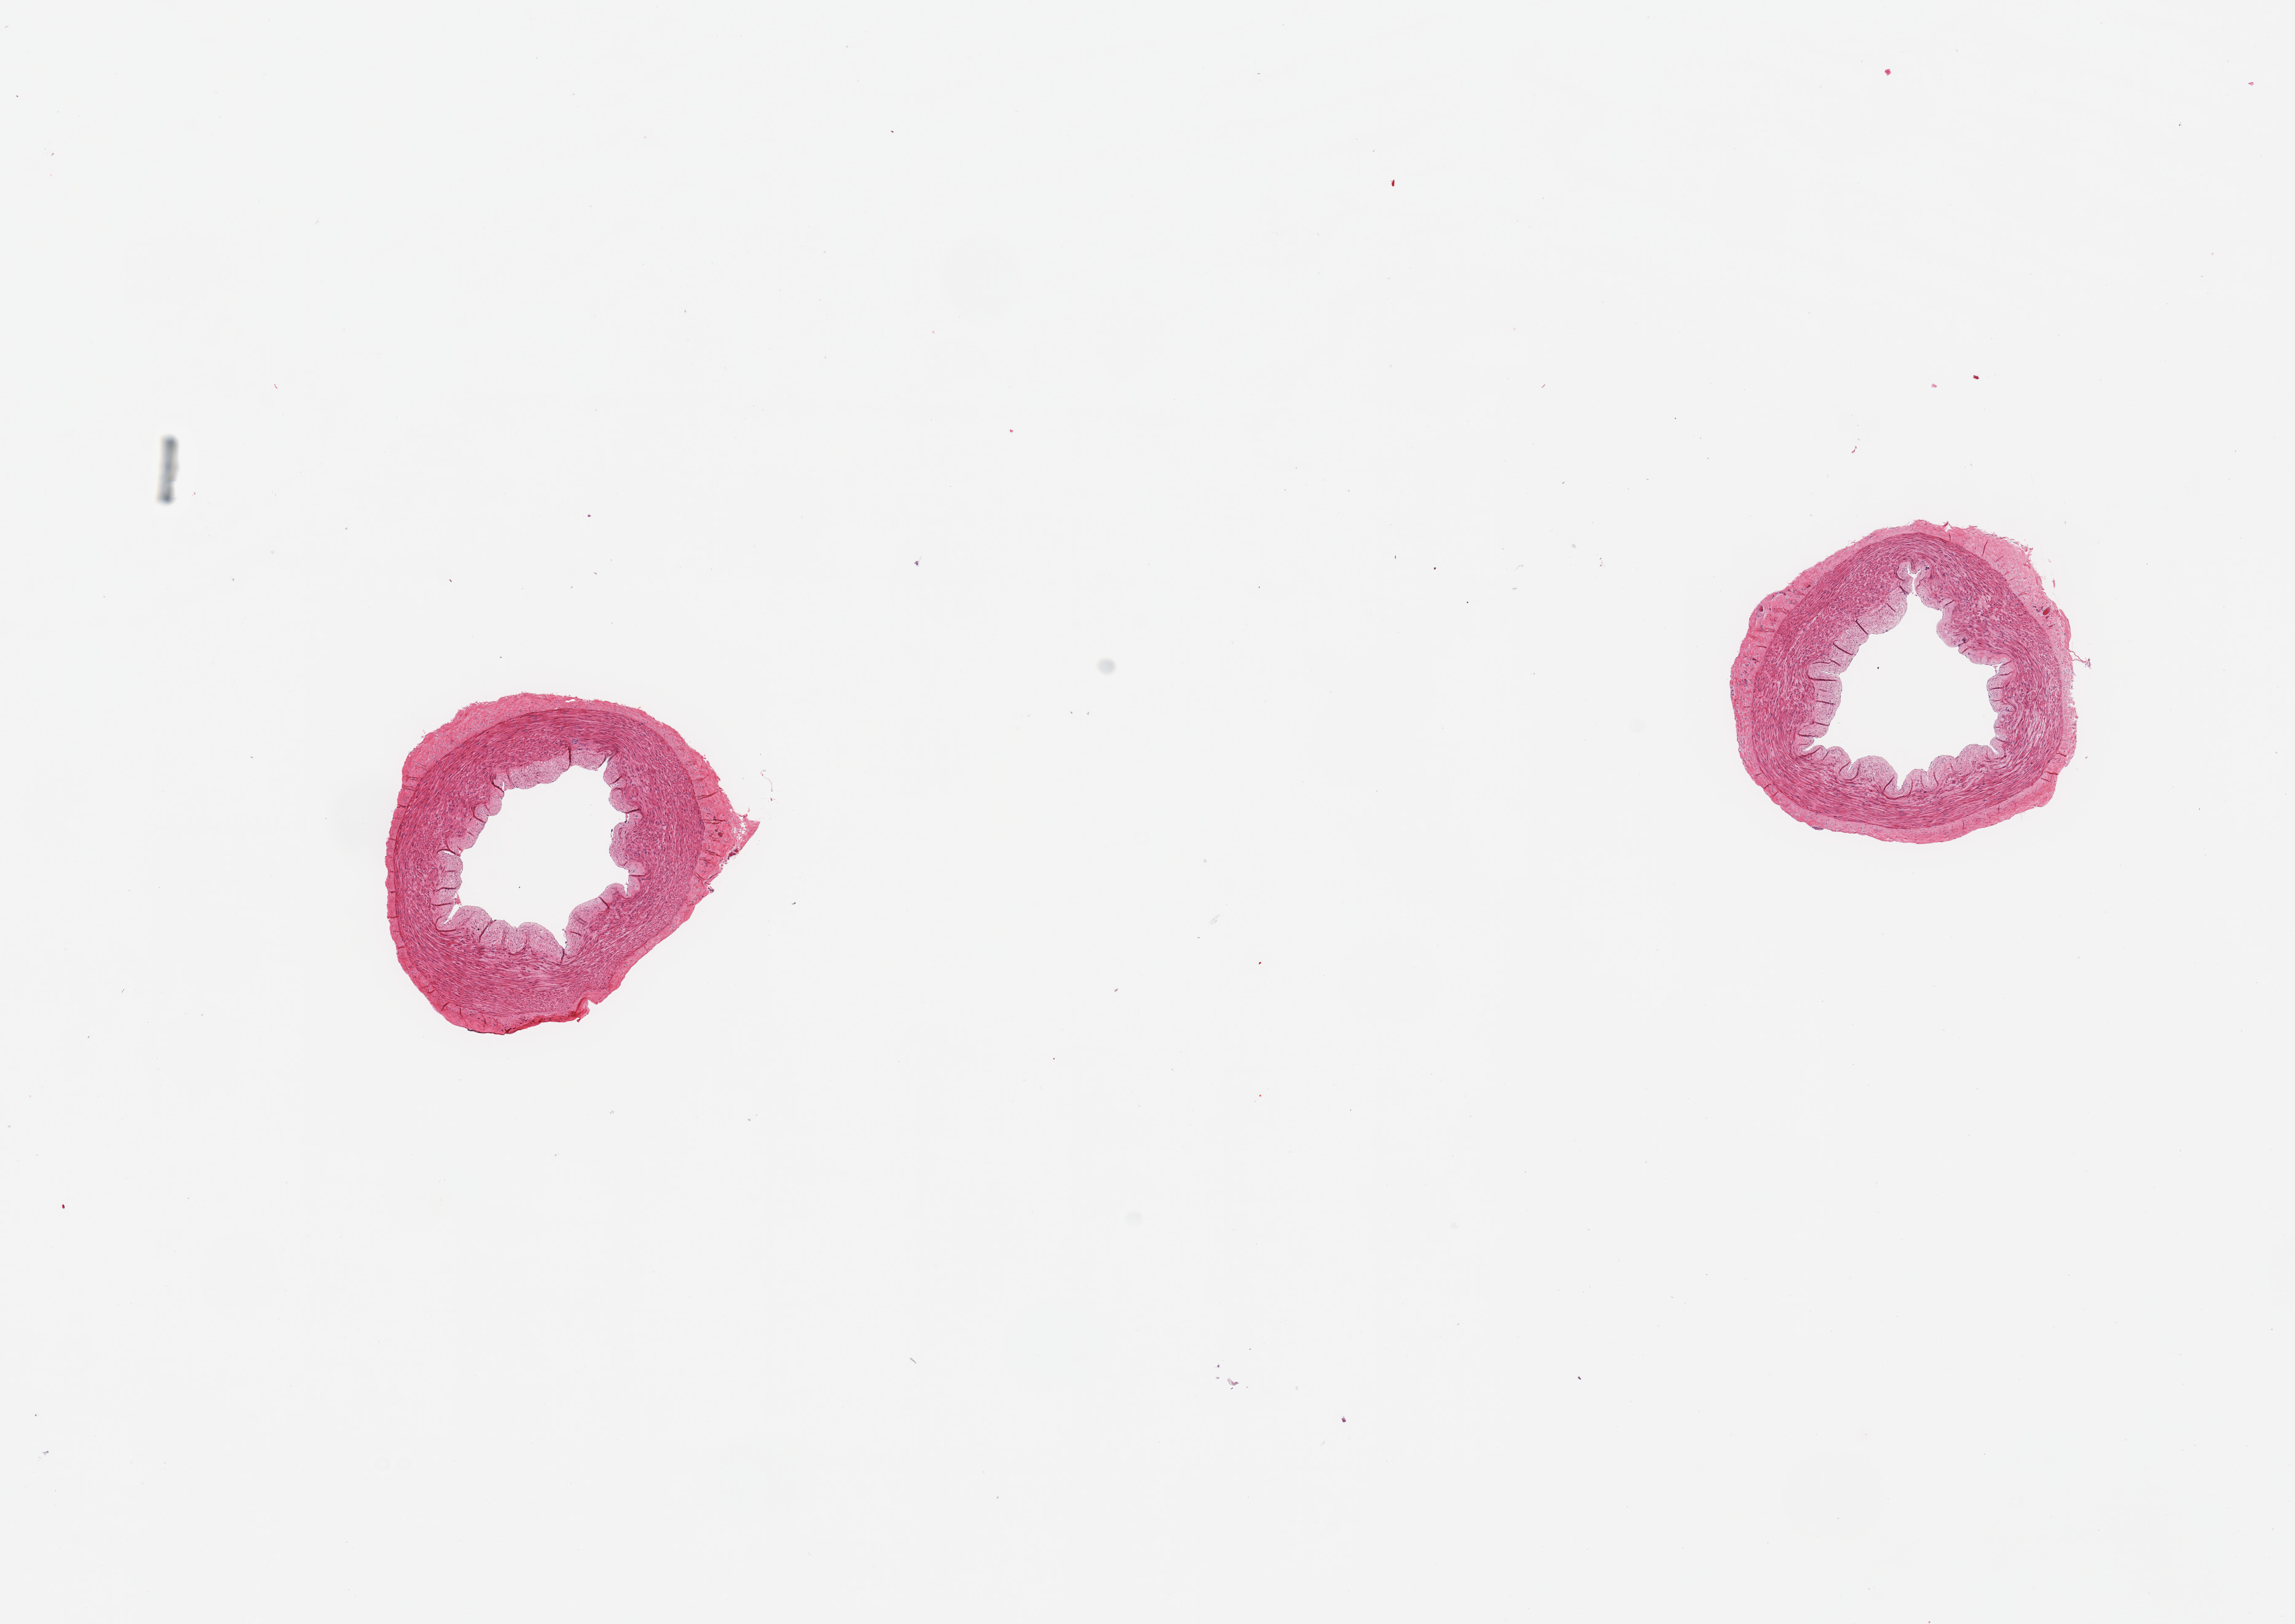
Hematoxylin and eosin (H&E) whole-slide image — shown as a low-resolution overview of the whole scanned area (about 14.8 x 10.4 mm, from a 20x scan), PAXgene-fixed, paraffin-embedded tissue, section of tibial artery (target tissue), tissue donor sample. Donor sex: male.
Pathologist's review note for this sample: 2 pieces; well trimmed.